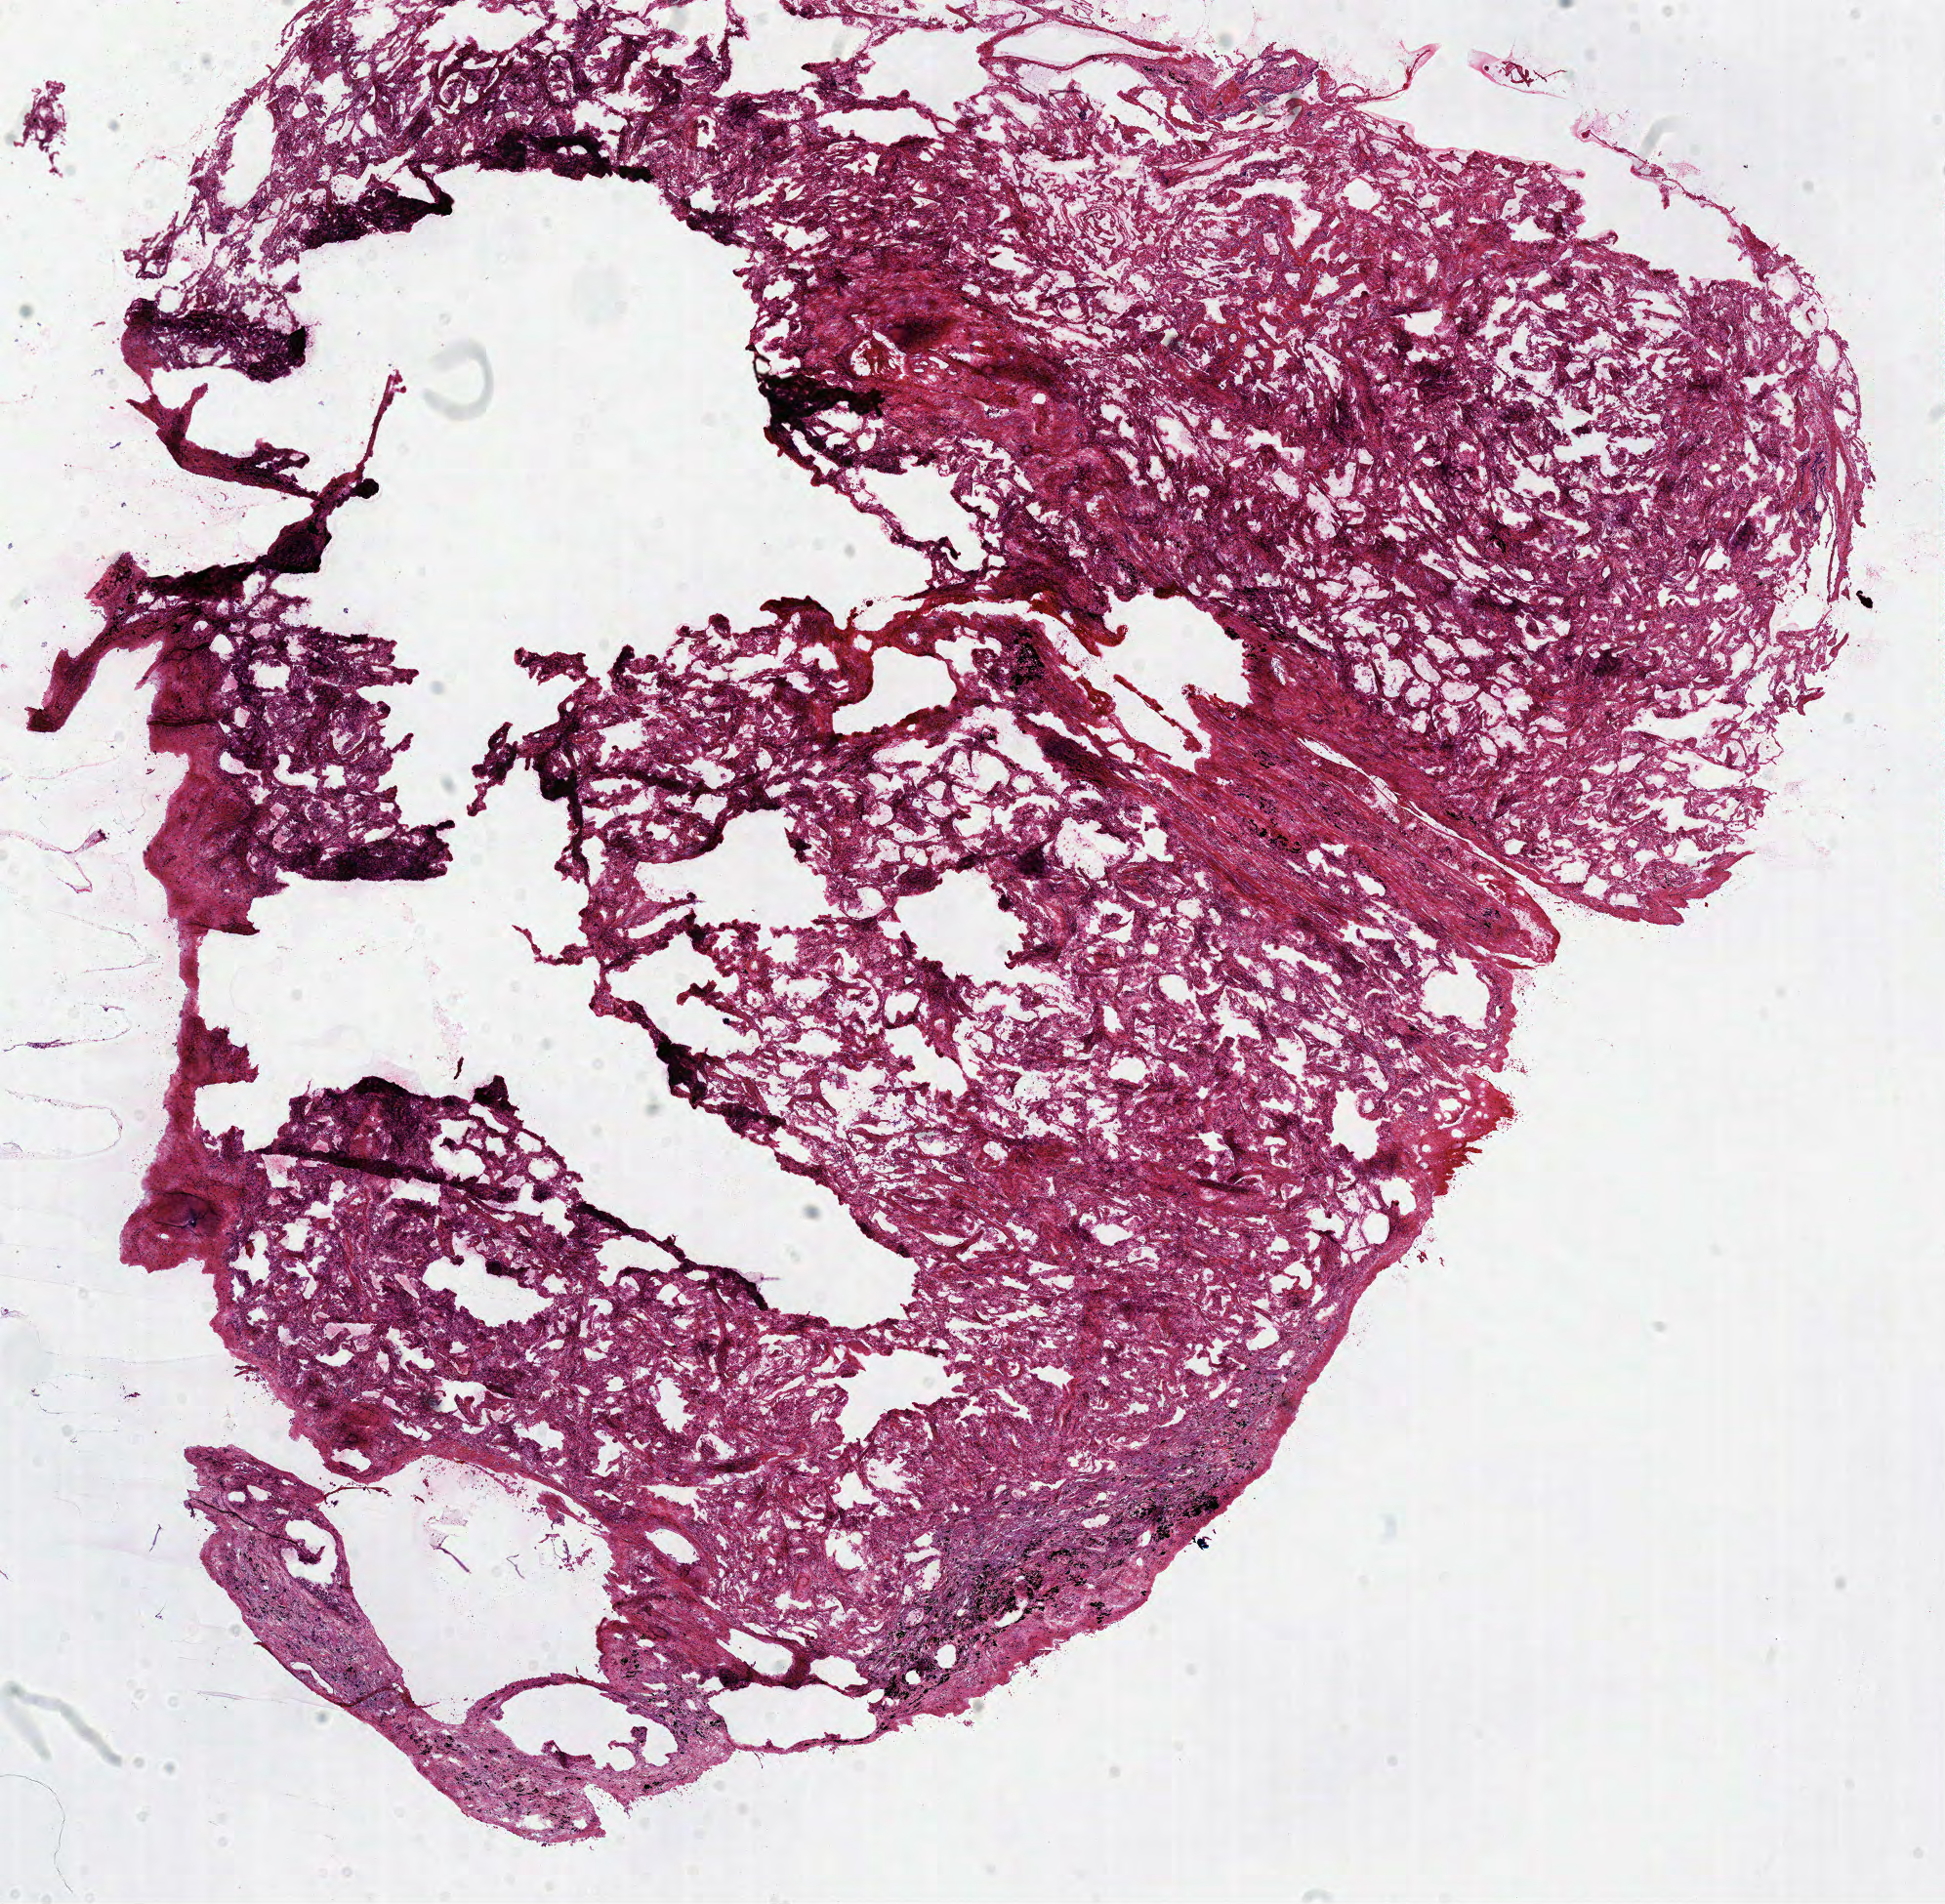
Digitized Hematoxylin and eosin (H&E) stained tissue section (whole slide), low-resolution overview of the scanned area, about 15.7 x 15.3 mm (from a 40x scan). Frozen section. Lung, solid tissue normal (non-tumour tissue) sample. Female, age 78 years at initial diagnosis.
This section: solid tissue normal (non-tumour) sample from the same patient. Patient diagnosis: Squamous cell carcinoma, NOS (upper lobe, lung).